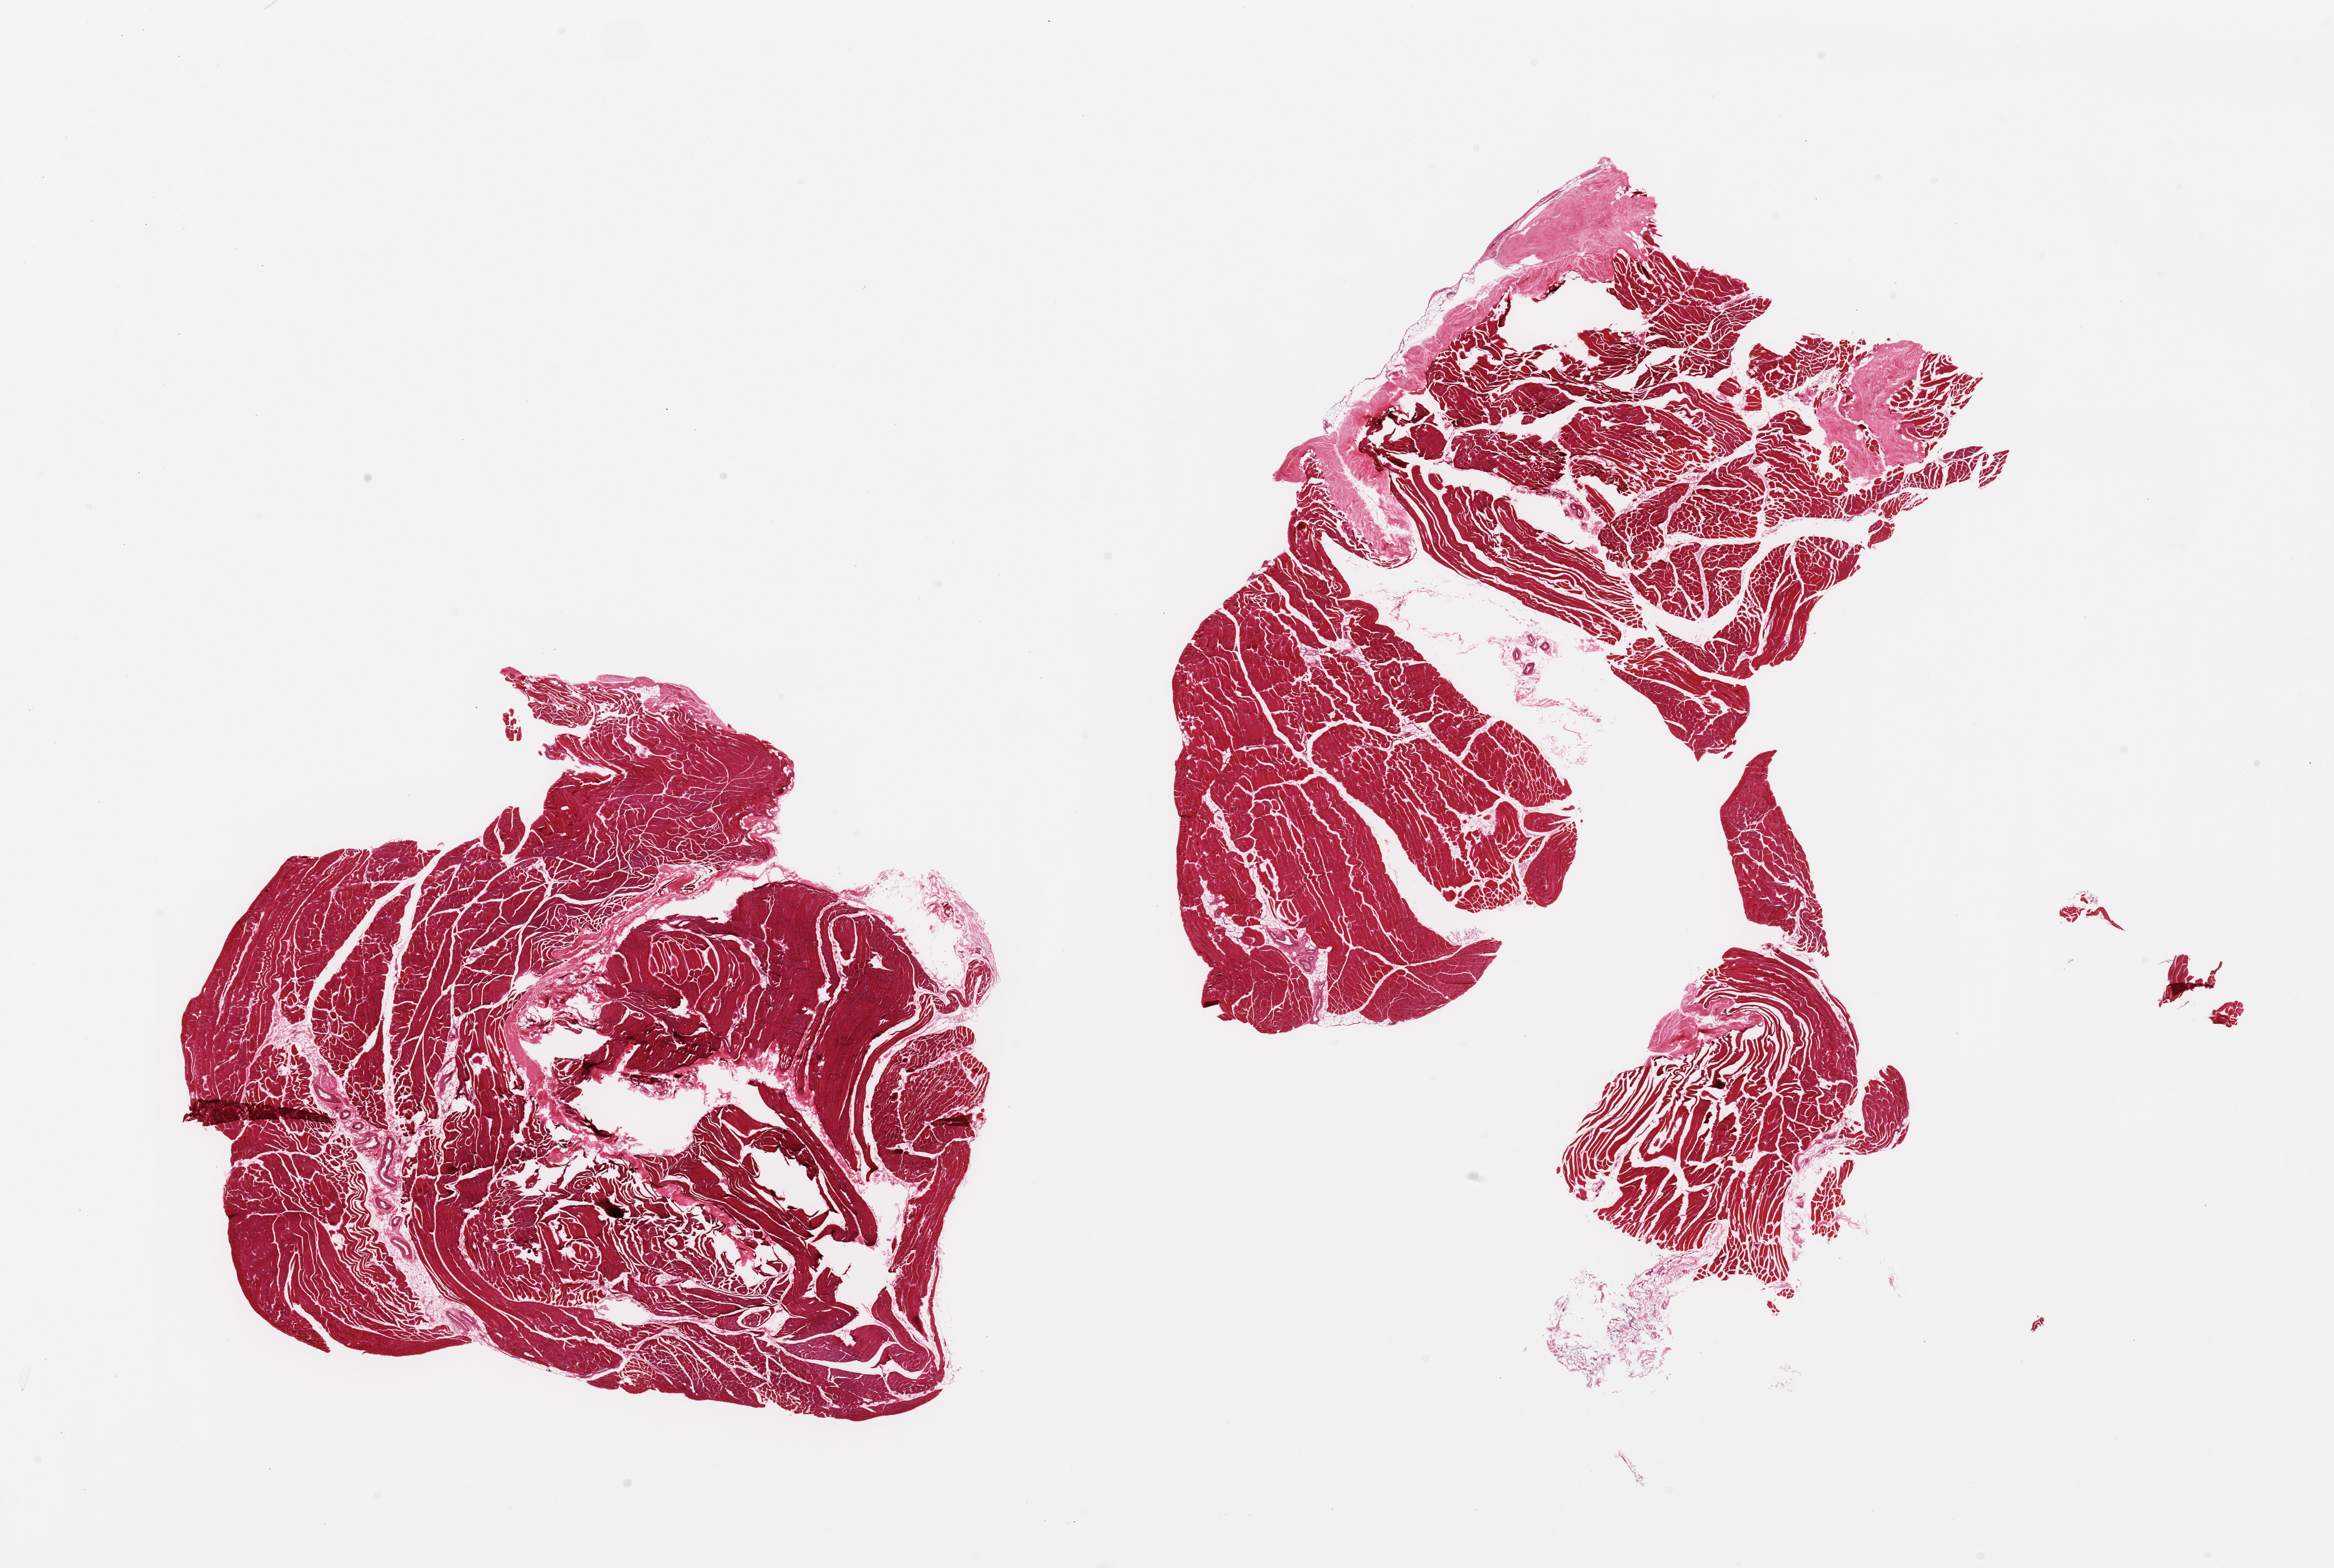
Whole-slide image, H&E stain — low-resolution overview of the scanned area, about 29.5 x 19.8 mm. PAXgene-fixed, paraffin-embedded tissue. Target tissue: skeletal muscle. Donor tissue sample. Female donor.
Pathologist's review note for this sample: 2 partly fragmented pieces; minimal extraneous tissue.